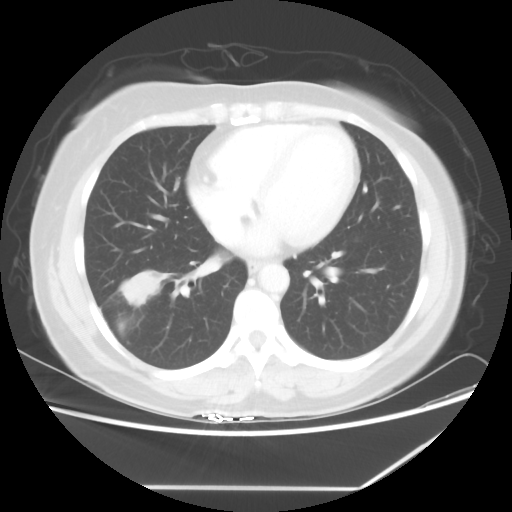
Chest CT, one axial slice. Slice 25 of 60 in the series (ordered by position). Reconstruction kernel STANDARD. 100 kVp. Lung window (W 1500 / L -600 HU). 5 mm slice thickness. 512 × 512 image matrix, field of view 374 × 374 mm. Patient: female, 42 years. Case-level facts recorded for this patient, not image findings: clinical TNM (as recorded): T2 N1 M0.
Outlined on this slice (rectangle marked by the reading radiologist):
- lung tumour (recorded histology: adenocarcinoma): bounding box (x1, y1, x2, y2) in pixels: (114, 262, 169, 306)